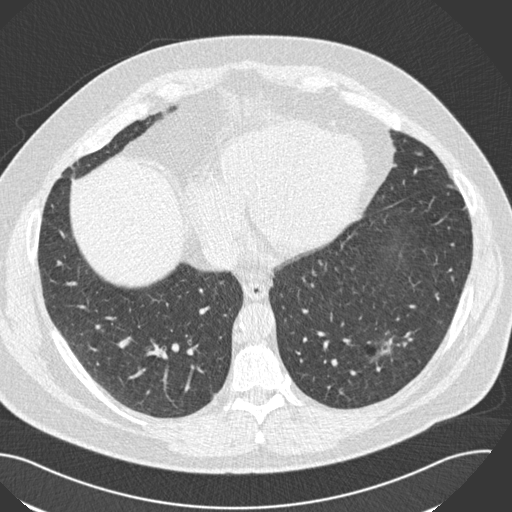
Low-dose screening chest CT, one axial slice; position 63 of 153 along the scan axis; reconstruction kernel B30f; lung window (W 1500 / L -600 HU); 2 mm slice thickness; 512 × 512 image matrix.
Structures marked on this image (expert manual segmentation):
- lesion 1 (tumor, lower lobe of left lung): bounding box <385,339,392,352> (left, top, right, bottom; pixels)